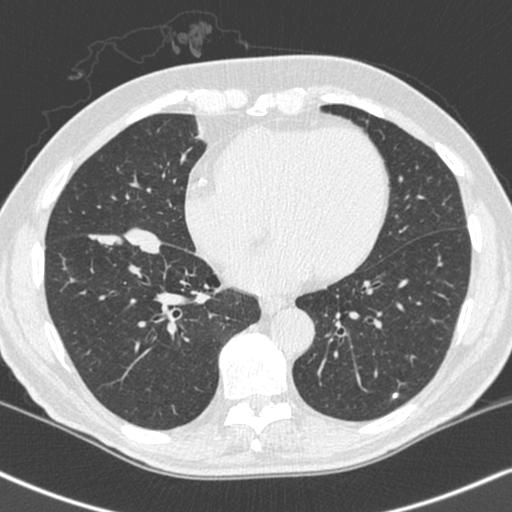
Chest CT (low-dose screening protocol), one axial image, baseline annual screen, lung window (W 1500 / L -600 HU), 1.3 mm slice thickness, standard (soft-tissue) reconstruction kernel (C), slice 143 of 248 in the series, 512 × 512 image matrix, field of view 323 × 323 mm. Male participant, aged 68 years at enrolment. Current smoker at enrolment.
Expert-annotated lung lesion, bounding box [x1, y1, x2, y2] px = [88, 225, 163, 296]. Reader record for this screening exam (exam-level; its link to the box is not recorded): non-calcified nodule or mass ≥4 mm, right lower lobe, 34 × 17 mm, smooth margins, soft tissue attenuation. Later outcome: lung cancer diagnosed 24 days after this screen — combined small cell carcinoma, right lower lobe, stage IIIA (AJCC 6th edition), 41 mm at pathology.